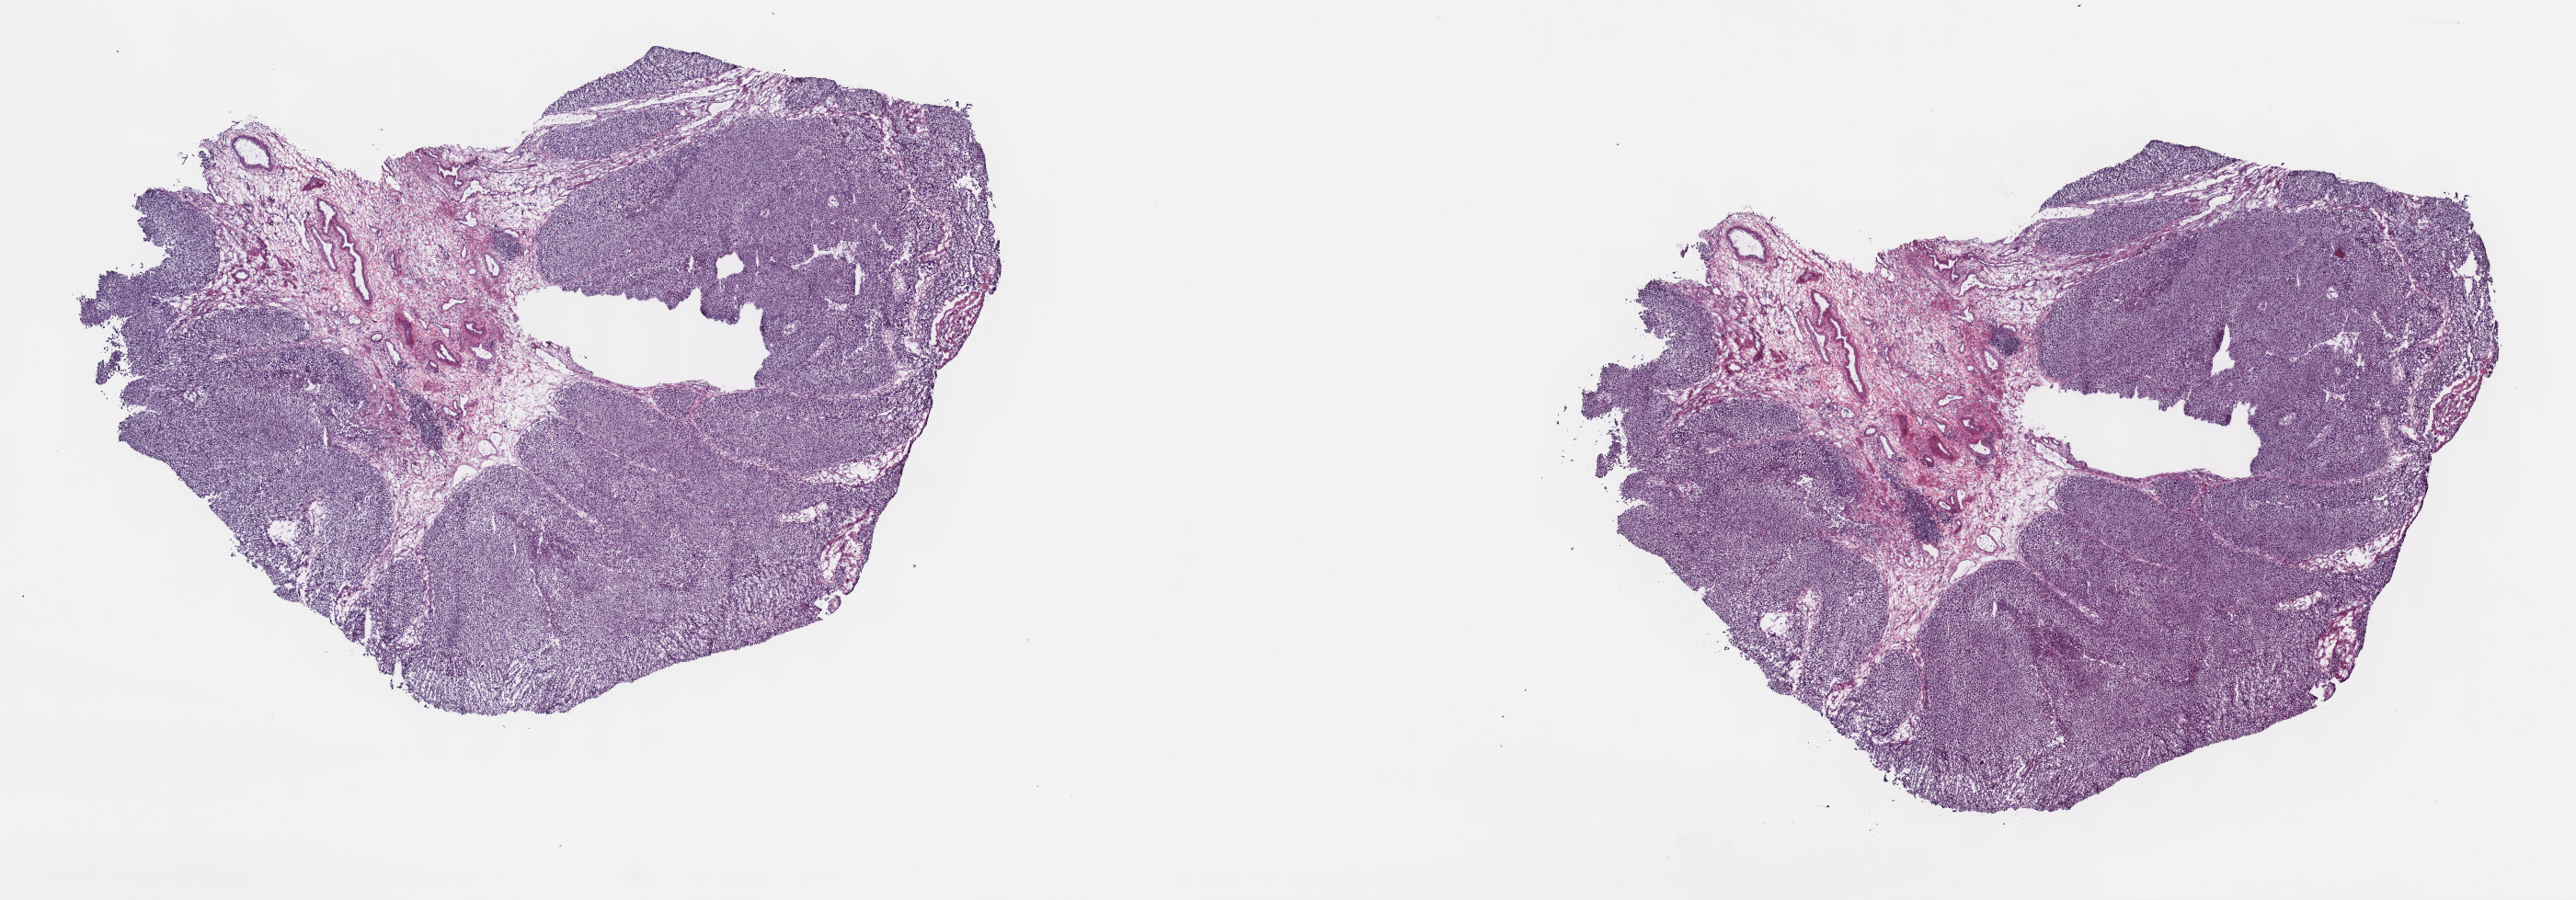
H&E-stained whole-slide image — low-resolution overview of the scanned area, about 22.7 x 7.9 mm (from a 40x scan); frozen section from the top of the tissue portion; sample: primary tumour, bladder. Male patient; age at initial diagnosis 66 years. Histologic grade: high grade. Slide review estimates, as recorded: tumour cells 80%, tumour nuclei 70%, normal cells 20%, stromal cells 0%, necrosis 0%. Inflammatory infiltration, as recorded: lymphocyte infiltration 4%, monocyte infiltration 0%, neutrophil infiltration 0%.
Lymph nodes positive (case pathology): 0 of 22 examined. AJCC pathologic stage: III (7th edition). Pathologic diagnosis: Papillary transitional cell carcinoma.